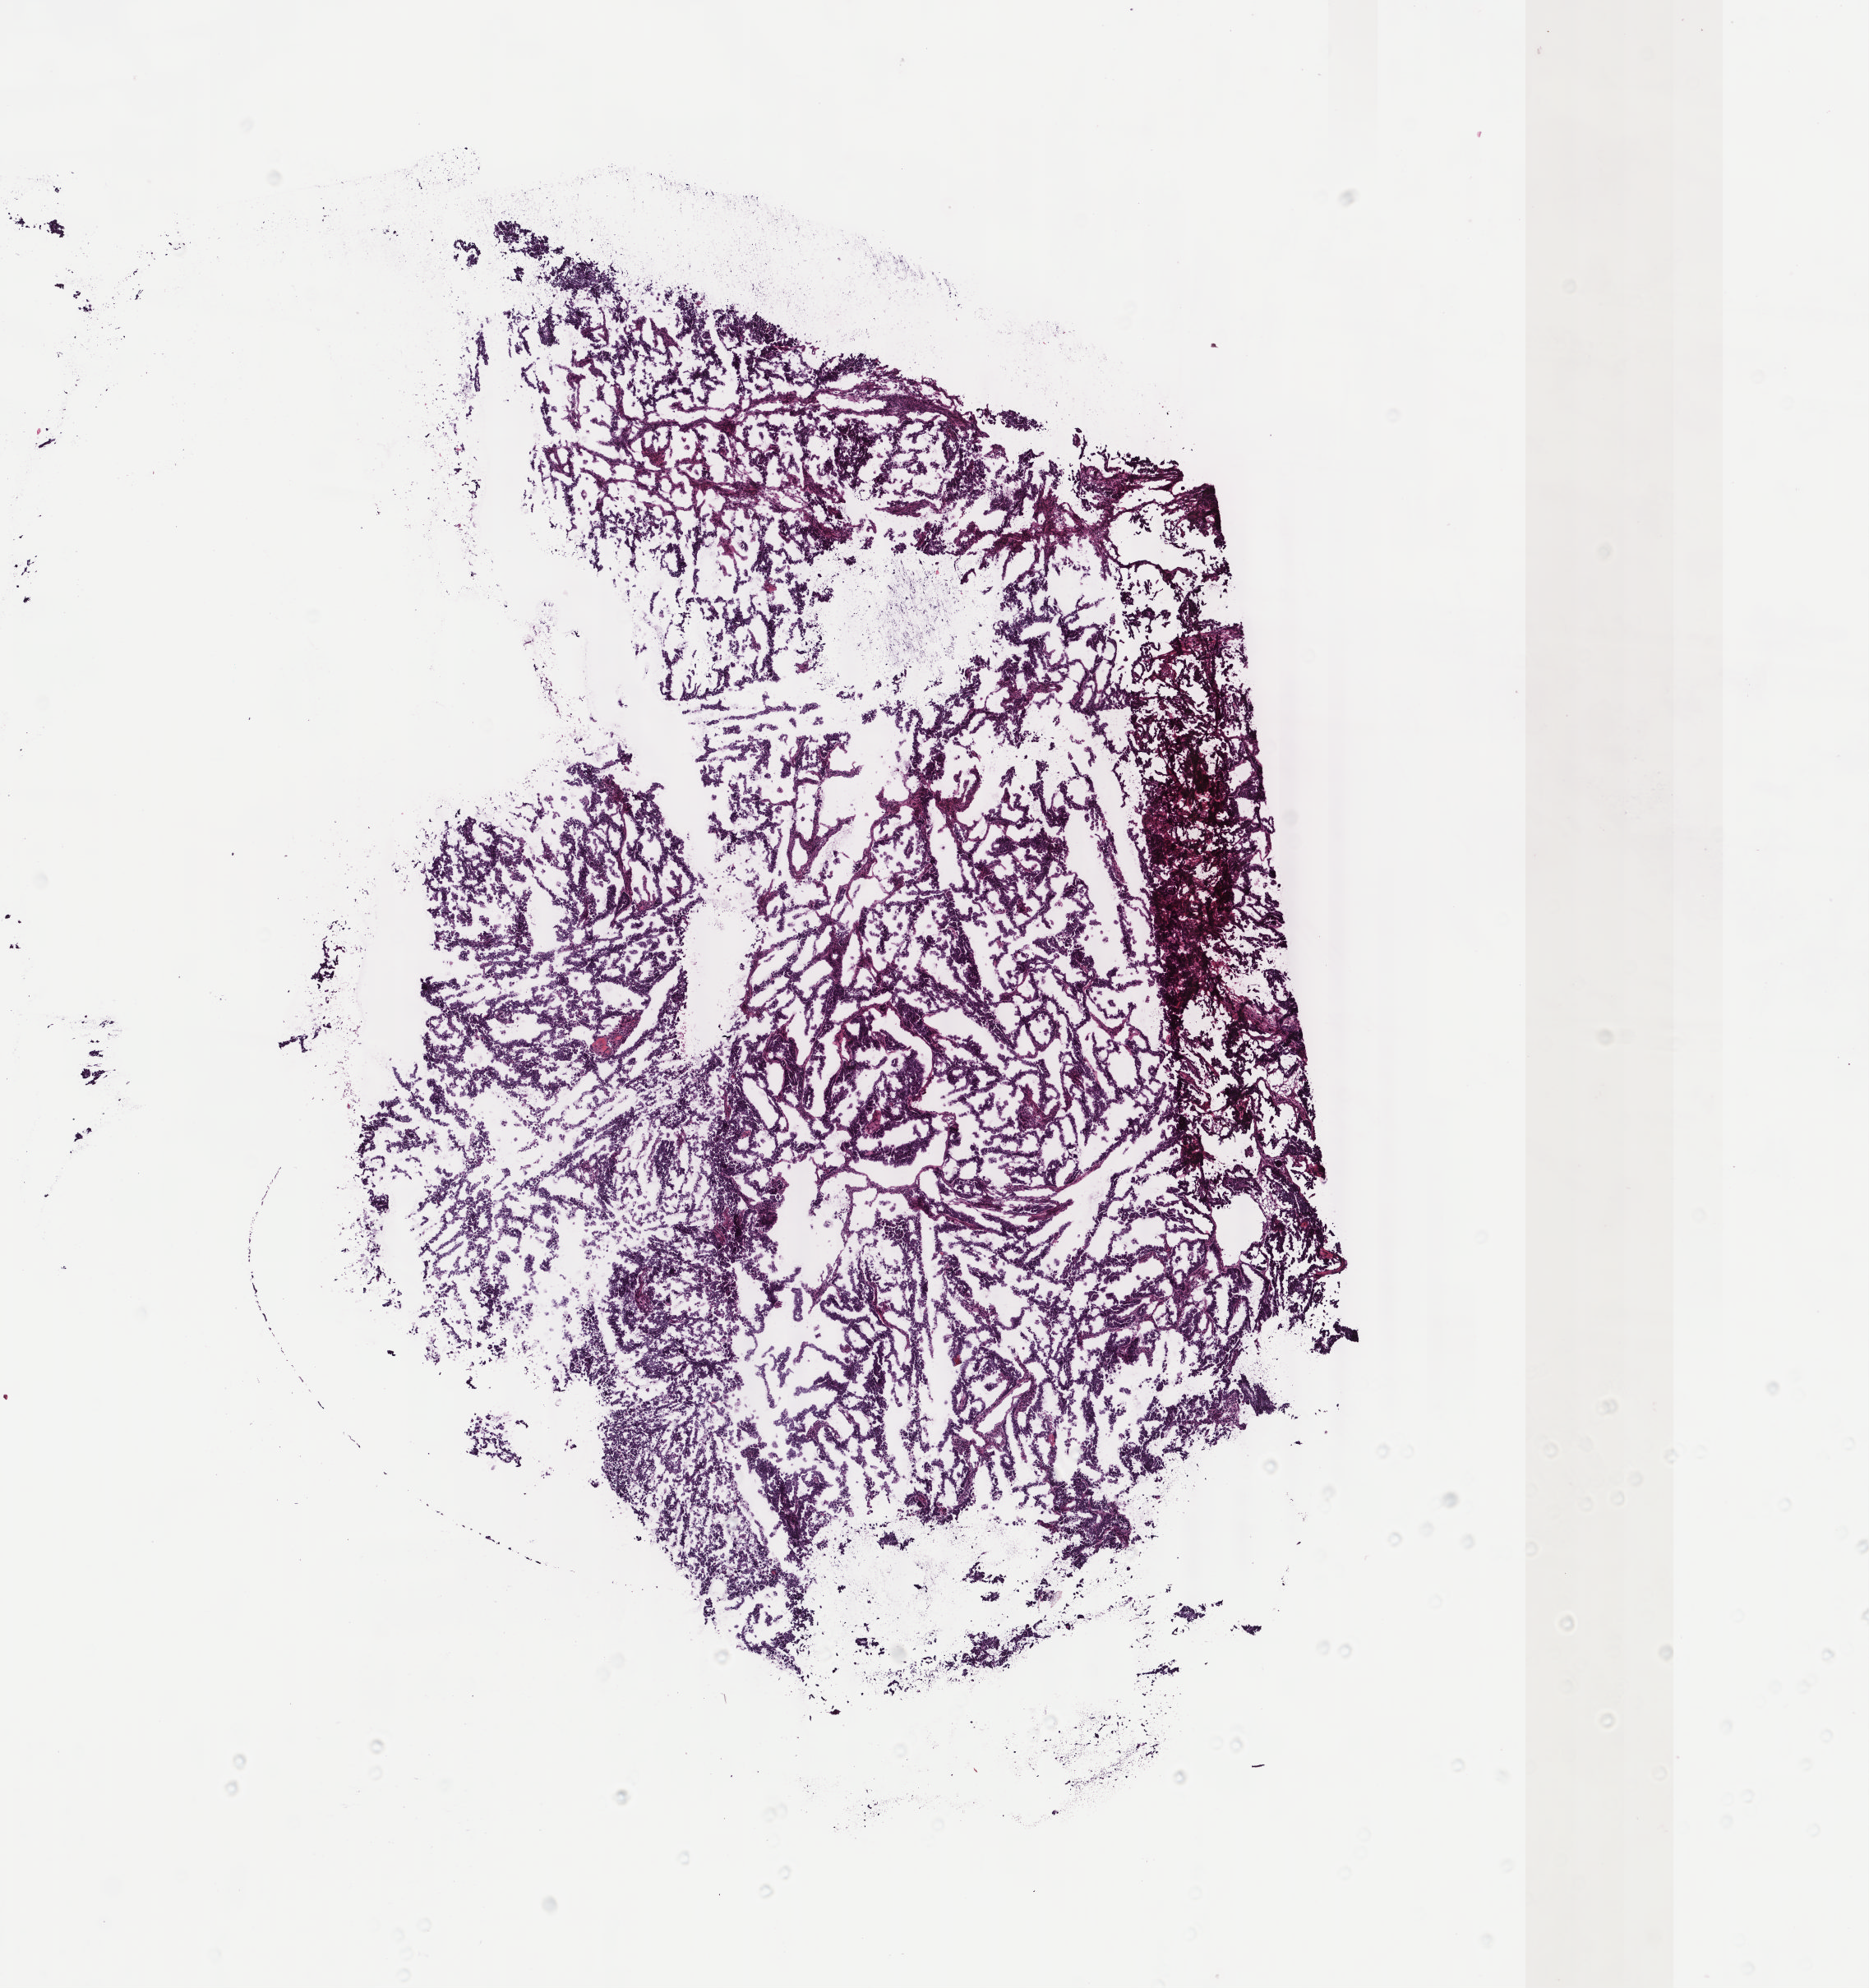
Whole-slide histology image, H&E, a low-resolution overview of the entire scanned area, about 9.0 x 9.6 mm (from a 40x scan); frozen section from the top of the tissue portion; primary tumour sample from the uterus. Female patient; age at initial diagnosis 67 years. Histologic grade: G3 (poorly differentiated). Pathologist review of this section (percent, as recorded): tumour cells 70%, tumour nuclei 75%, normal cells 0%, stromal cells 25%, necrosis 5%. Infiltration values recorded for this section: lymphocyte infiltration 15%, monocyte infiltration 0%, neutrophil infiltration 0%.
* FIGO stage: IIIA
* diagnosis: Serous cystadenocarcinoma, NOS (endometrium)